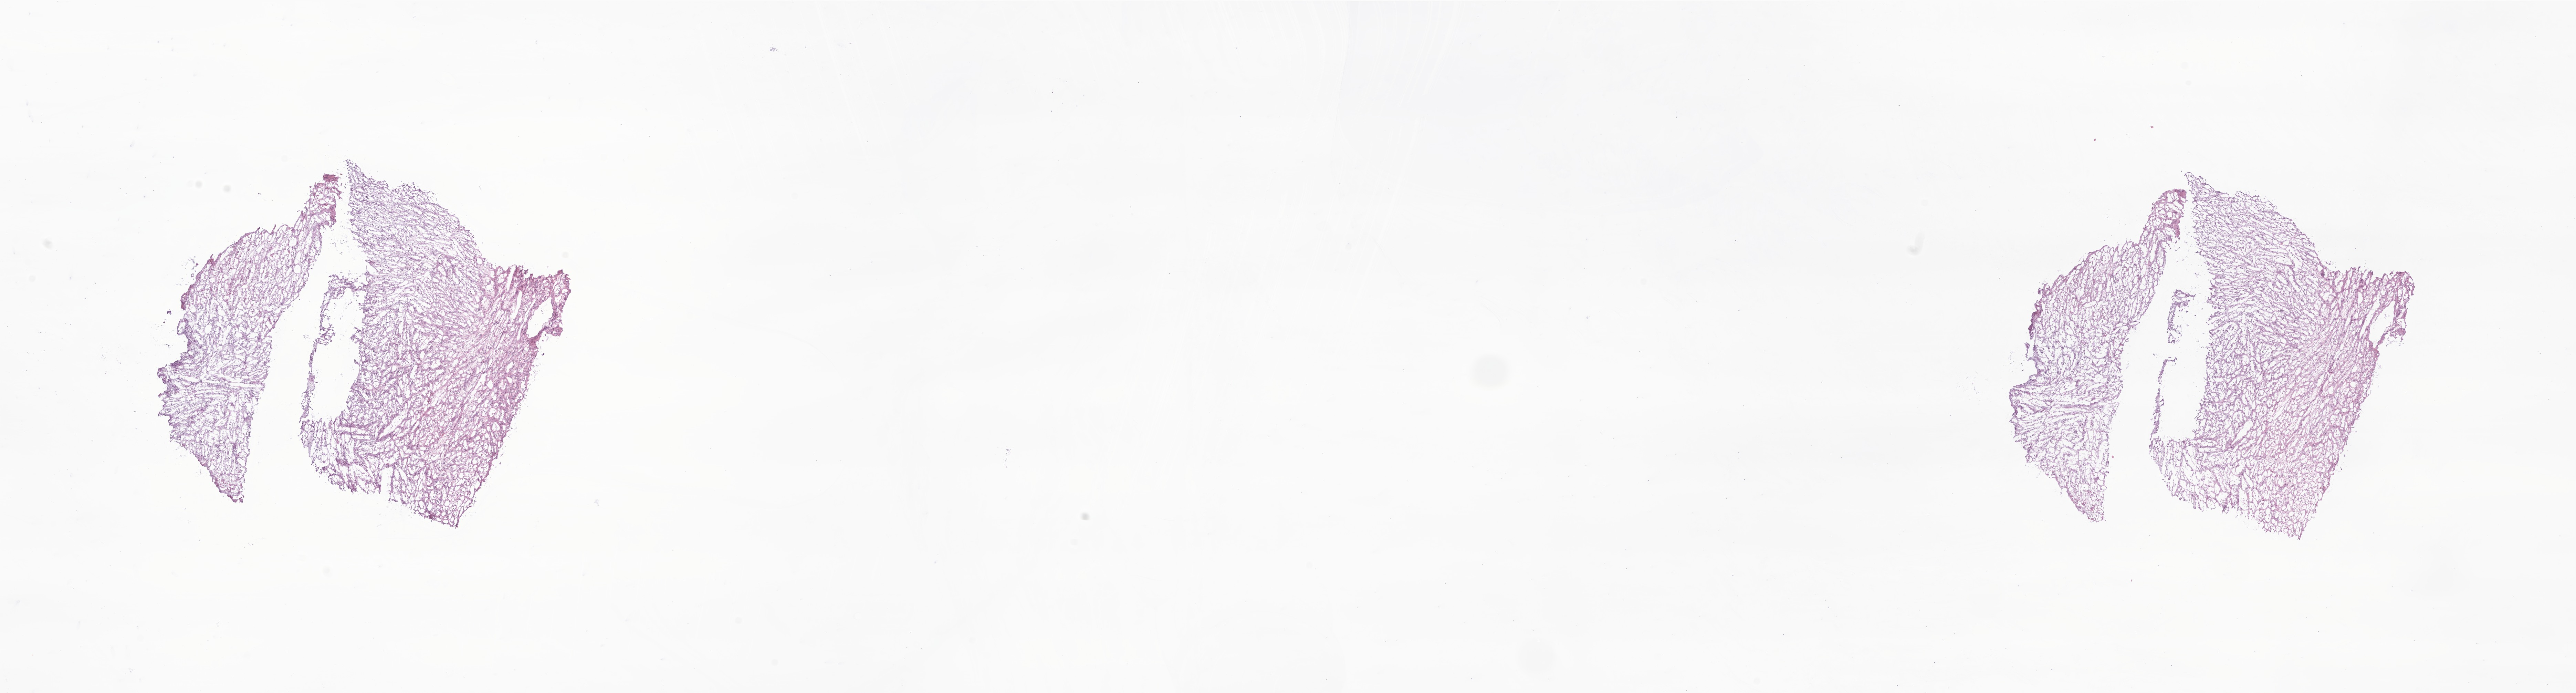
Haematoxylin and eosin whole-slide image of tumor tissue from the submandibular gland, shown as a low-resolution overview of the whole scanned area (about 31.5 x 8.5 mm); frozen section (OCT-embedded). Patient female; age 39 months (3 years 3 months).
Recorded diagnosis: Embryonal rhabdomyosarcoma, NOS.